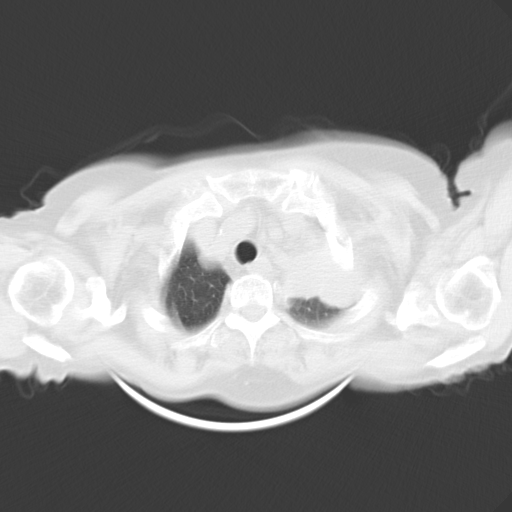
Chest CT, one axial slice; position 24 of 26 along the scan axis; reconstruction kernel B40f; 120 kVp; lung window (W 1500 / L -600 HU); 10 mm slice thickness; 512 × 512 image matrix. Patient: female, 71 years. Case-level facts recorded for this patient, not image findings: clinical TNM (as recorded): T3 N3 M0.
Annotated regions visible in this slice (bounding box drawn by a radiologist):
- lung tumour (recorded histology: adenocarcinoma): bounding box <275,231,360,321> (left, top, right, bottom; pixels)